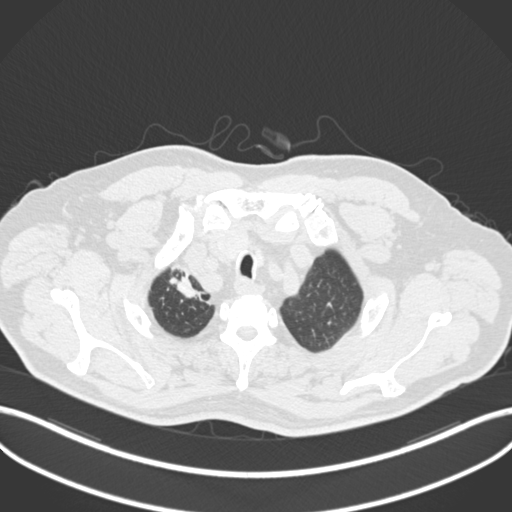
Chest CT, one axial slice. Position 183 of 255 along the scan axis. Reconstruction kernel B30f. Lung window (W 1500 / L -600 HU). 1 mm slice thickness. 512 × 512 image matrix, field of view 400 × 400 mm. Male patient, age 60 years. From the clinical record (not read from this slice): clinical TNM (as recorded): T1b N1 M0.
Structures marked on this image (rectangle marked by the reading radiologist):
- lung tumour (recorded histology: squamous cell carcinoma): bounding box <167,267,209,307> (left, top, right, bottom; pixels)